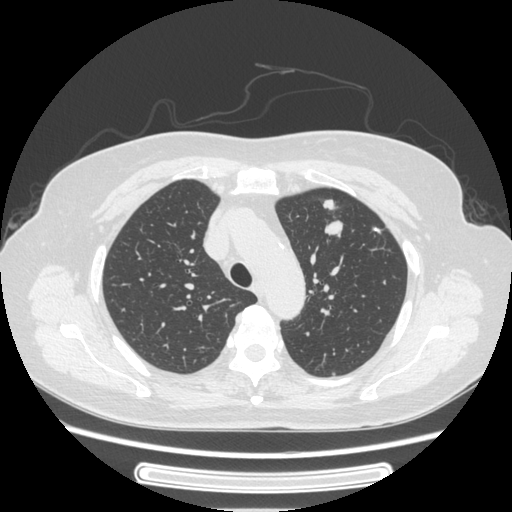
Chest CT, one axial slice; position 178 of 227 along the scan axis; reconstruction kernel STANDARD; lung window (W 1500 / L -600 HU); 1.25 mm slice thickness; 512 × 512 image matrix, field of view 363 × 363 mm. Female patient, age 77 years. Case-level facts recorded for this patient, not image findings: clinical TNM (as recorded): T1c N3 M0; histopathological grade: G2-3.
Structures marked on this image (rectangle marked by the reading radiologist):
- lung tumour (recorded histology: adenocarcinoma): bounding box <319,192,346,248> (left, top, right, bottom; pixels)